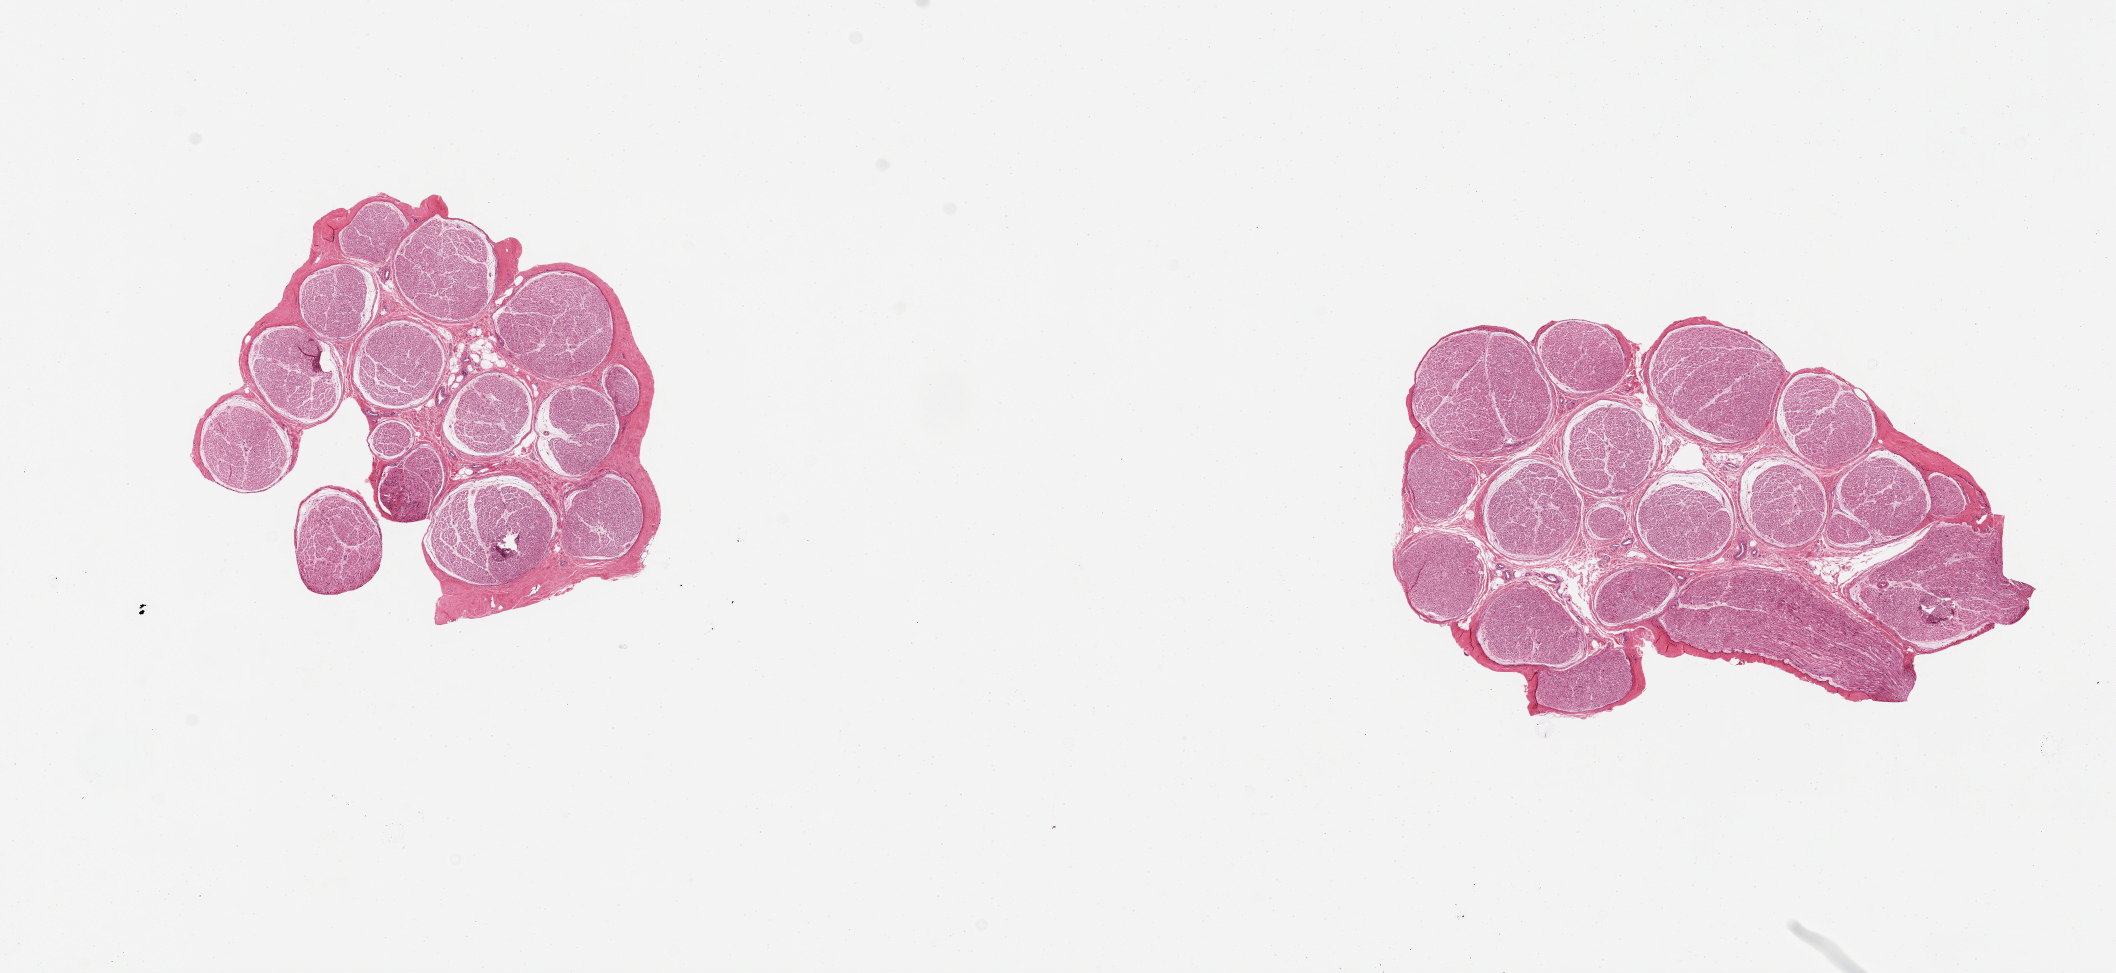
Digitized hematoxylin and eosin (H&E)-stained section, shown as a low-resolution overview of the whole scanned area (about 16.7 x 7.7 mm). PAXgene-fixed, paraffin-embedded tissue. Sampled site (target tissue): tibial nerve. Donor tissue sample. Donor sex: male.
Reviewer comment on this tissue sample: 2 pieces, clean specimens, no adherent fat.